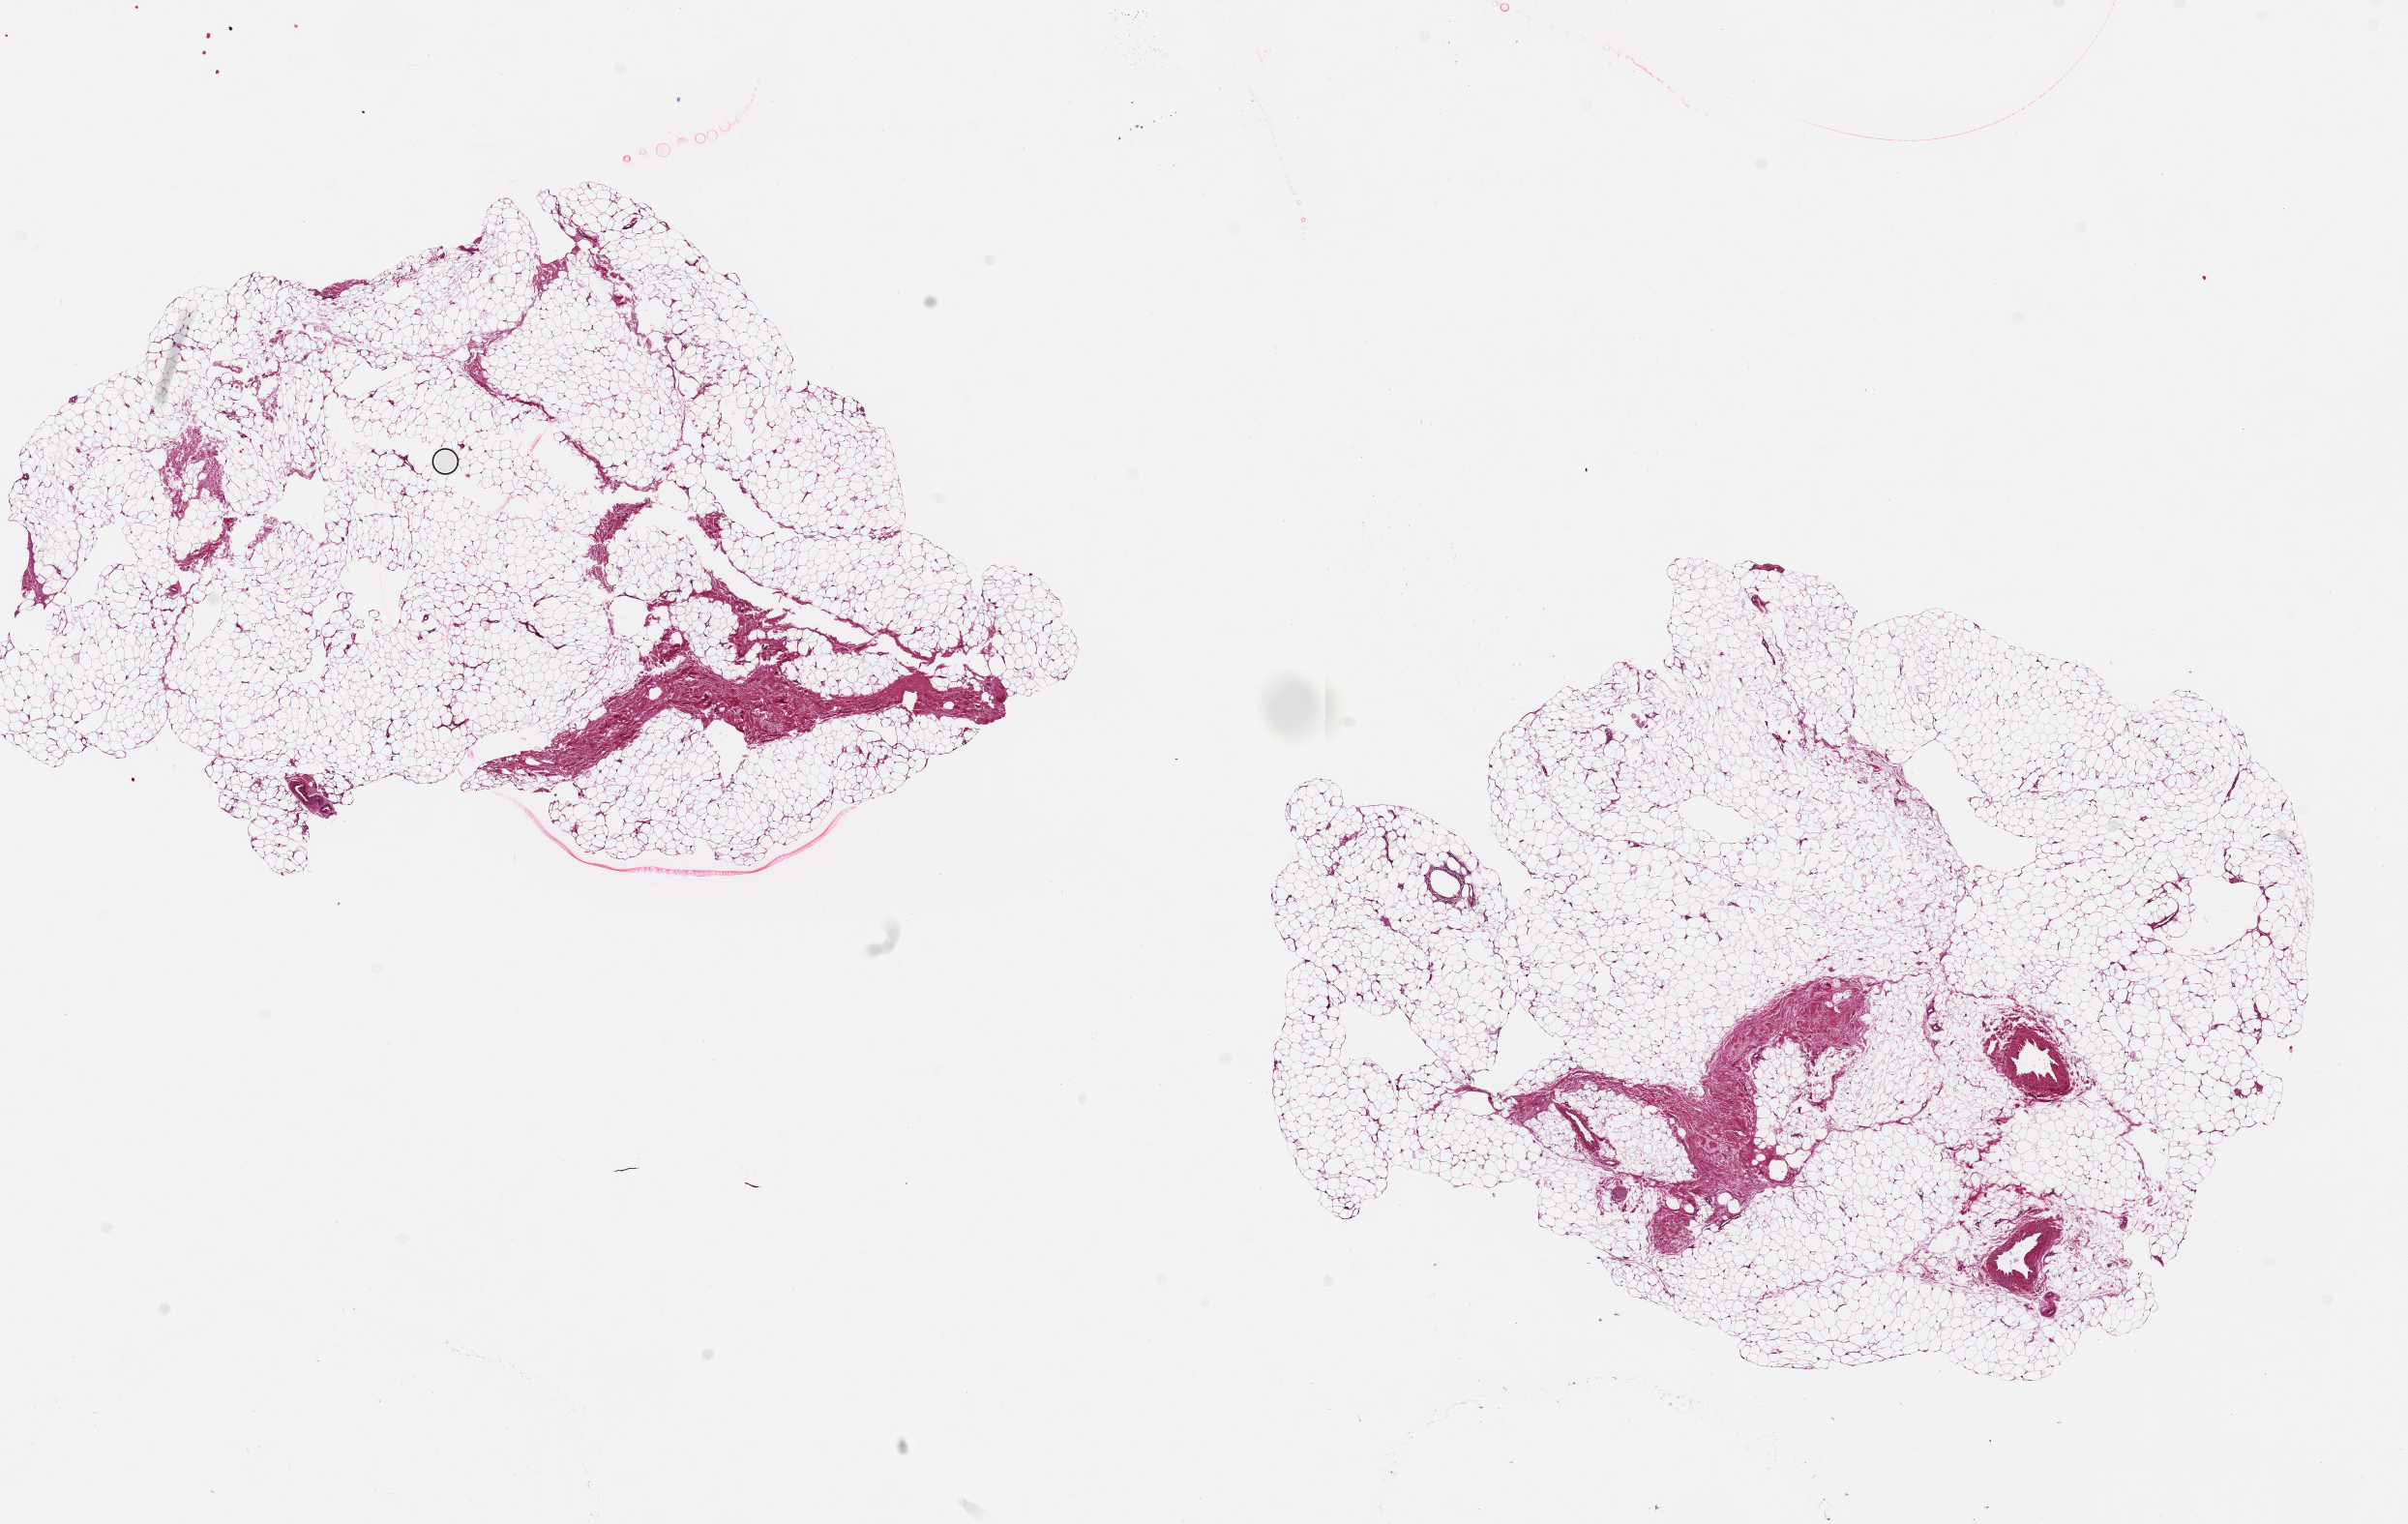
Digitized hematoxylin and eosin (H&E)-stained section, shown as a low-resolution overview of the whole scanned area (about 19.7 x 12.5 mm); PAXgene-fixed, paraffin-embedded tissue; target tissue: adipose tissue; donor tissue sample. Donor sex: male.
Pathologist's review note for this sample: 2 aliquots, ~9x5mm.